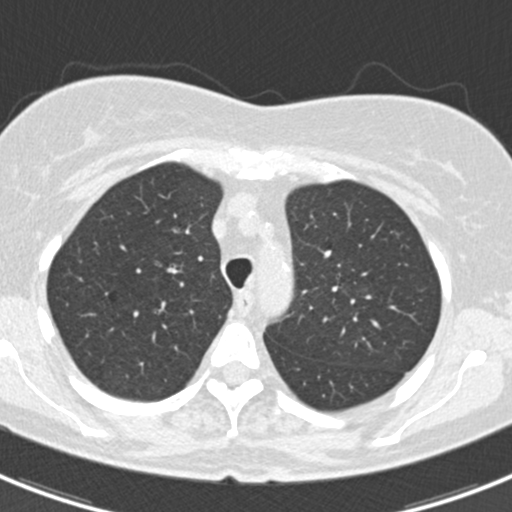
Chest CT (low-dose screening protocol), one axial image, baseline screening round, lung window (W 1500 / L -600 HU), standard (soft-tissue) reconstruction kernel (B30f), slice 51 of 184 in the series, 512 × 512 image matrix. Female participant, aged 60 years at enrolment. Current smoker at enrolment.
• Expert reader's lesion annotation, box from (x=372, y=222) to (x=418, y=254) px.
• The screening reader recorded 3 non-calcified nodules or masses ≥4 mm on this exam (lingula, left lower lobe, lingula); which of them this box marks is not recorded.
• Official screen result: positive, change unspecified: nodule(s) >= 4 mm or enlarging nodule(s), mass(es), or other non-specific abnormalities suspicious for lung cancer.
• Lung cancer was diagnosed 886 days after this screen: non-small cell carcinoma, left upper lobe, poorly differentiated (G3), stage IB (AJCC 6th edition), 7 mm at pathology.